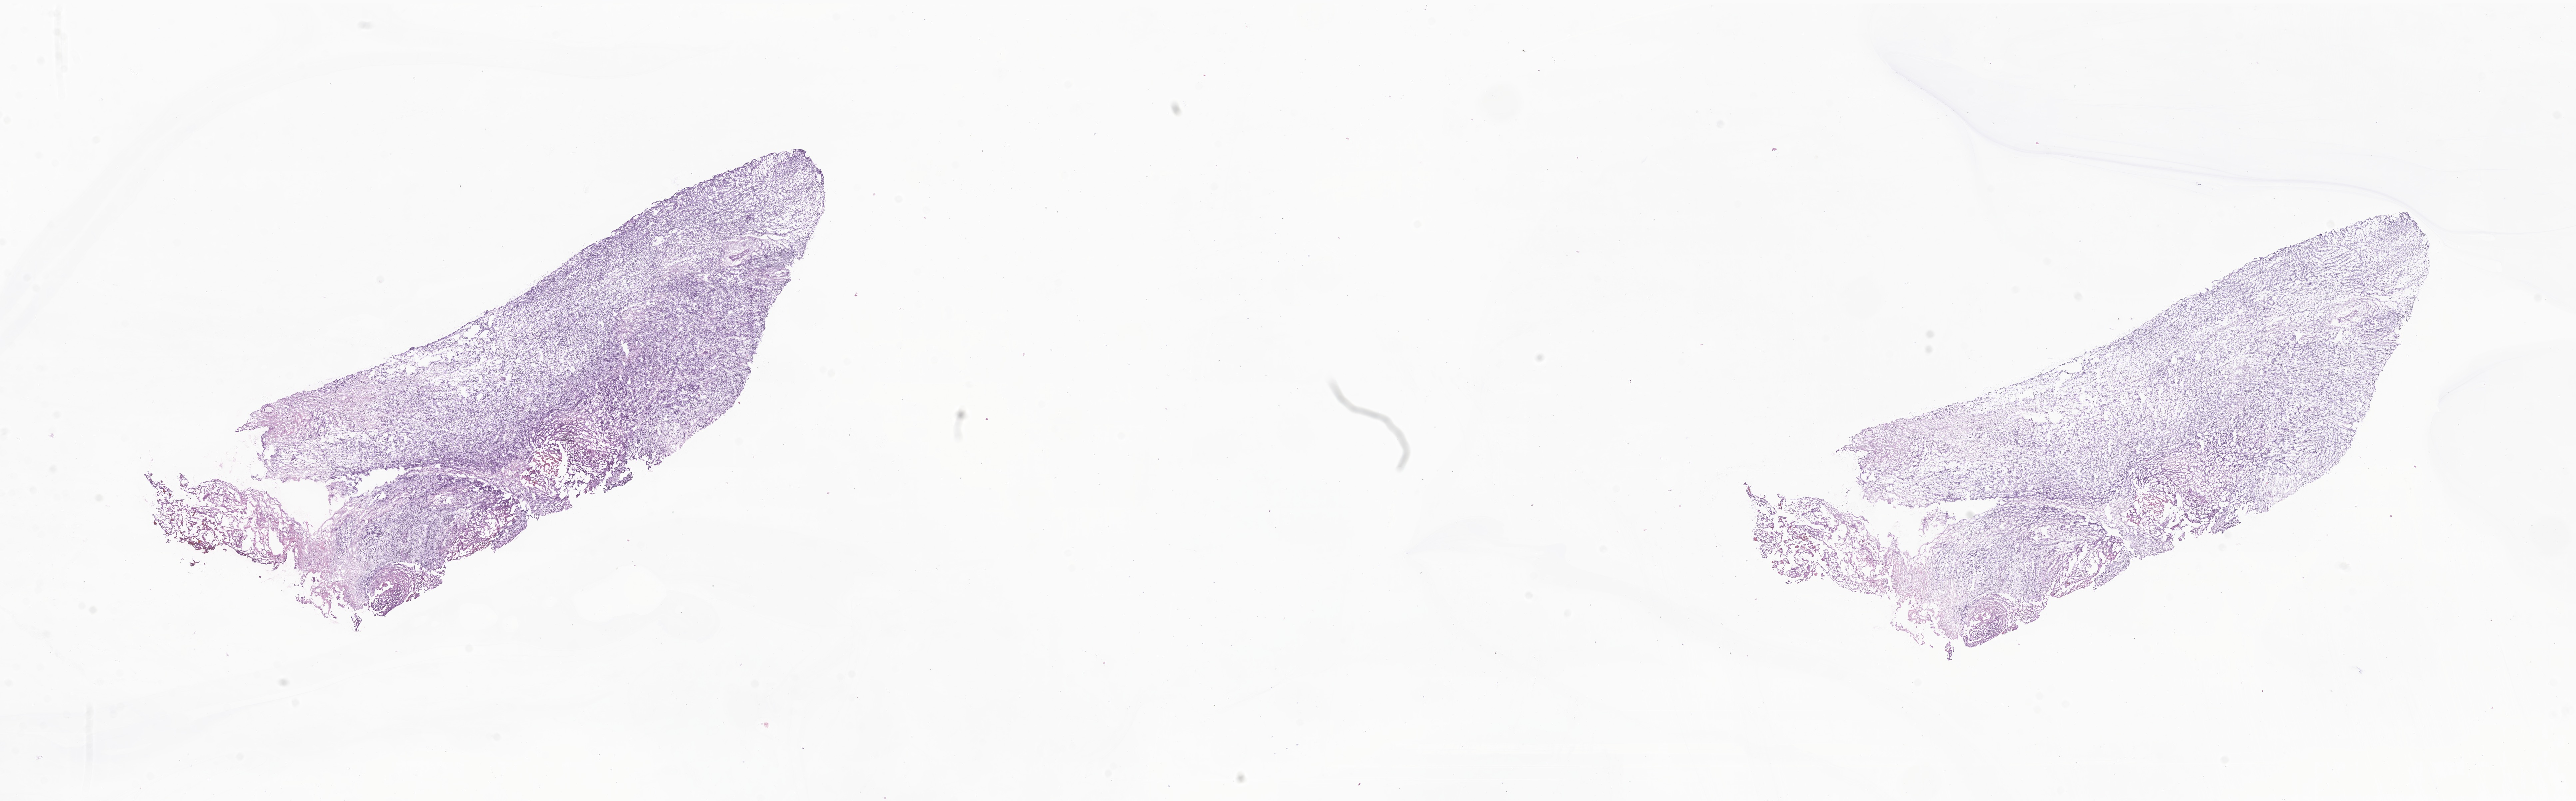
Whole-slide image, haematoxylin and eosin stain of tumor tissue from the orbit, a low-resolution overview of the entire scanned area, about 32.6 x 10.1 mm. Frozen section. Patient: male, age 92 months.
Diagnosis (ICD-O-3 morphology term): Spindle cell rhabdomyosarcoma.